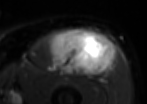
MRI of an extremity soft-tissue mass, one axial slice; slice 46 of 85 in the series (ordered by position); T2-weighted fat-saturated; MR volume resampled by the dataset authors to the PET/CT grid (not the native acquisition matrix); 3.27 mm slice thickness; 147 × 104 image matrix, field of view 144 × 102 mm. Male patient. From the clinical record (not read from this slice): histological type: extraskeletal osteosarcoma; grade: high; site of the primary tumour: thigh.
Outlined on this slice (expert contour drawn on MRI and transferred to this co-registered scan by the dataset authors):
- gross tumour volume (mass): bounding box [x1, y1, x2, y2] px = [49, 28, 112, 75]